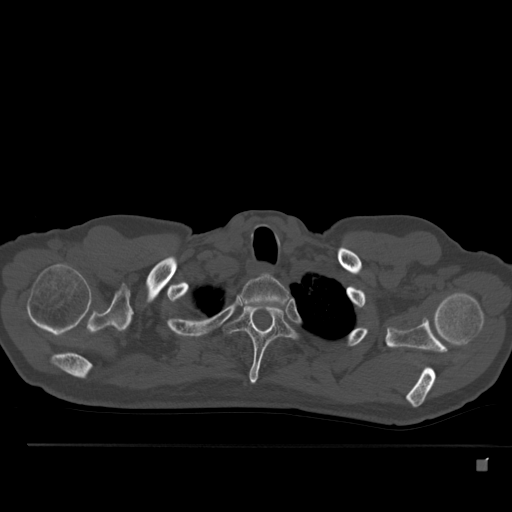
CT including the spine, one axial slice. Slice 415 of 517 in the series (ordered by position). 120 kVp. Bone window (W 1800 / L 400 HU). 512 × 512 image matrix. Male patient, age 70 years. From the clinical record (not read from this slice): primary cancer: renal.
Annotated regions visible in this slice (semi-automatic segmentation, software-assisted and operator-edited):
- T1 vertebra: bounding box [x1, y1, x2, y2] px = [242, 274, 289, 305]
- T2 vertebra: [223, 303, 296, 384]